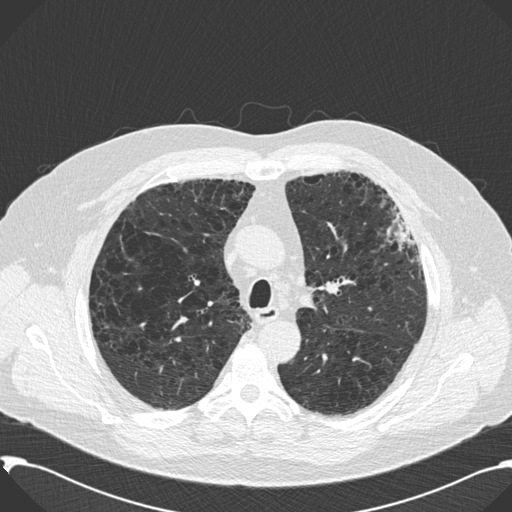
Chest CT (low-dose screening protocol), one axial image. Second annual screen. Lung window (W 1500 / L -600 HU). Slice 53 of 199 in the series. 512 × 512 image matrix, field of view 380 × 380 mm. Male, age 59 years at enrolment. Current smoker at enrolment.
- Expert reader's lesion annotation, bounding box <361,194,426,292> (left, top, right, bottom; pixels).
- No non-calcified nodule or mass ≥4 mm was recorded by the screening reader at this exam.
- Participant outcome: lung cancer diagnosed 518 days after this screen (after the third annual screen) — bronchiolo-alveolar carcinoma, mixed mucinous and non-mucinous, left upper lobe, stage IA (AJCC 6th edition), 20 mm at pathology.